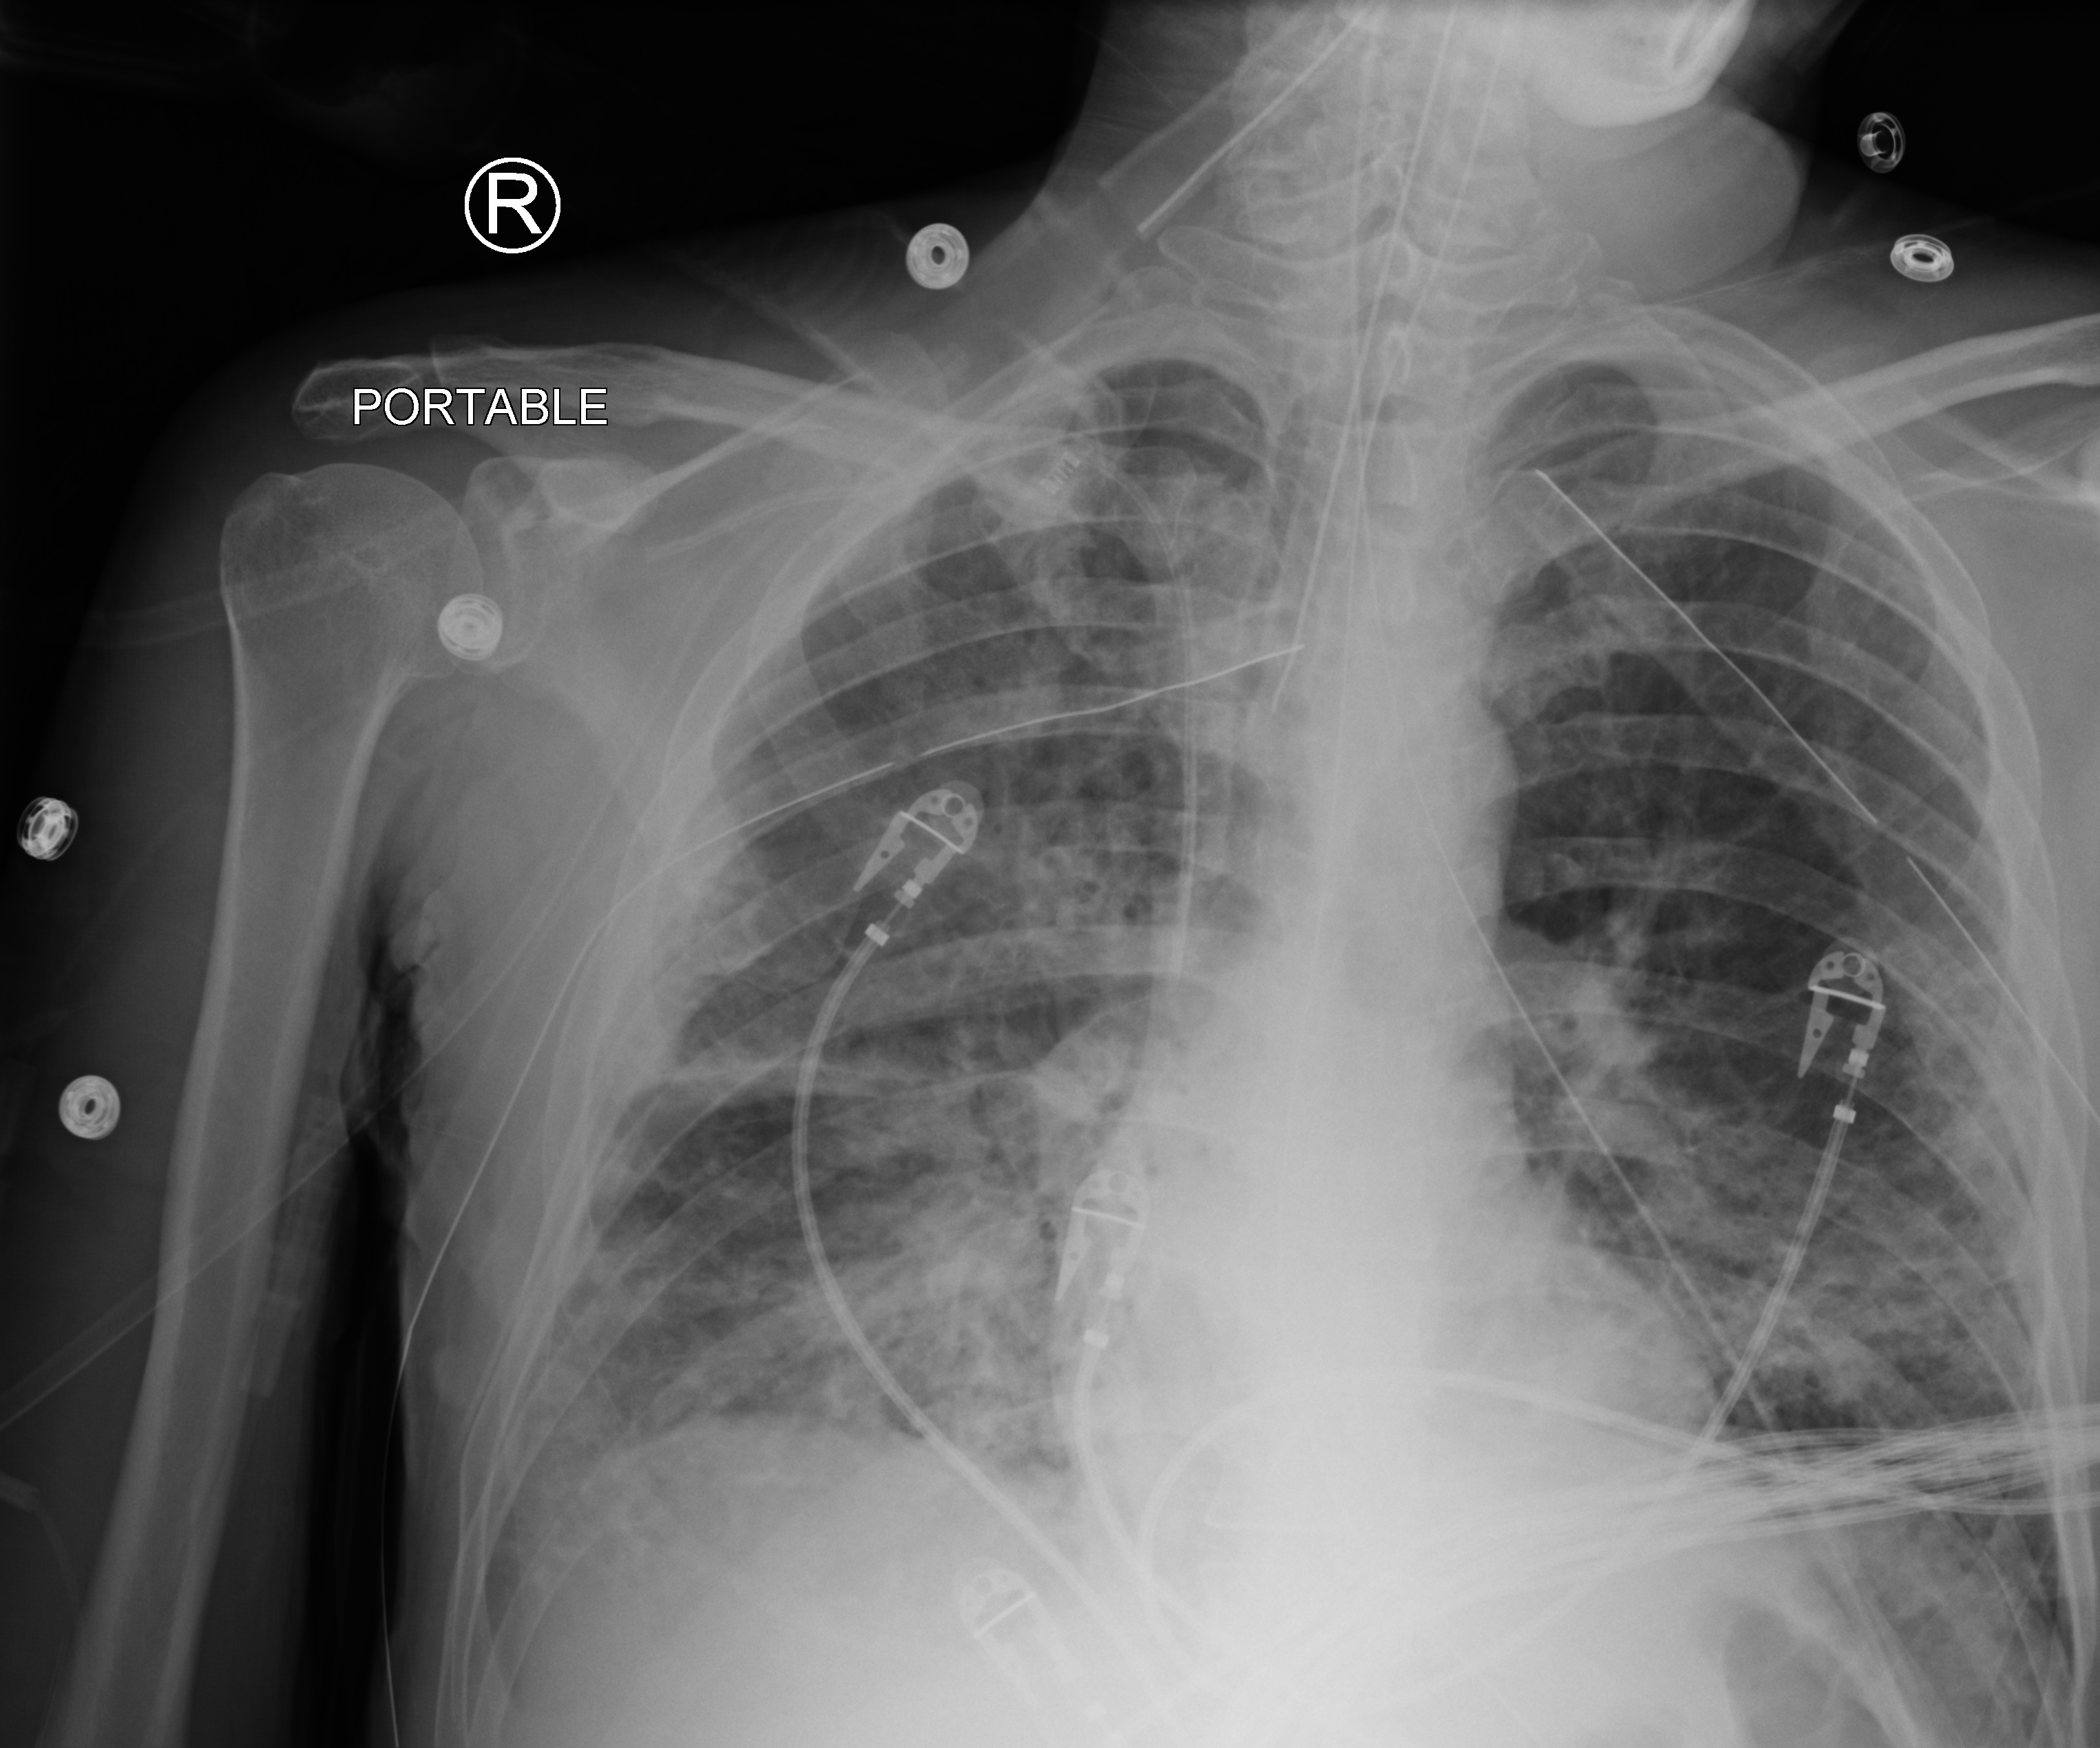
Bedside chest radiograph (computed radiography). Patient hospitalised with COVID-19; male, aged 18–59 years.
Hospital-stay facts (about this admission, not read from this image; timing relative to this image not recorded): admitted to intensive care during this hospital stay: yes.